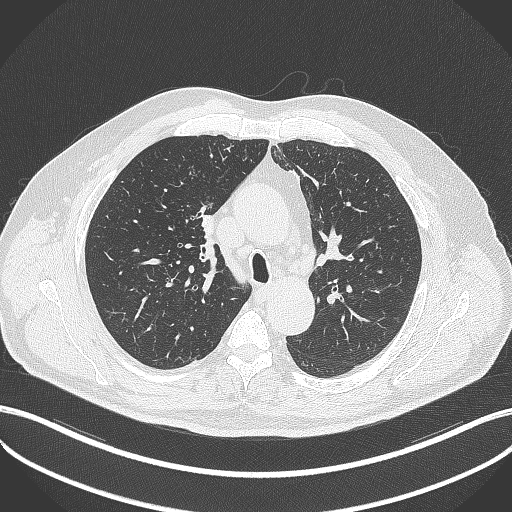
Chest CT, one axial slice. Slice 261 of 411 in the series (ordered by position). Reconstruction kernel B70f. 120 kVp. Lung window (W 1500 / L -600 HU). 512 × 512 image matrix. Male patient, age 60 years. Case-level facts recorded for this patient, not image findings: clinical TNM (as recorded): T1b N1 M0.
Structures marked on this image (rectangle marked by the reading radiologist):
- lung tumour (recorded histology: squamous cell carcinoma): bounding box (x1, y1, x2, y2) in pixels: (198, 207, 223, 246)